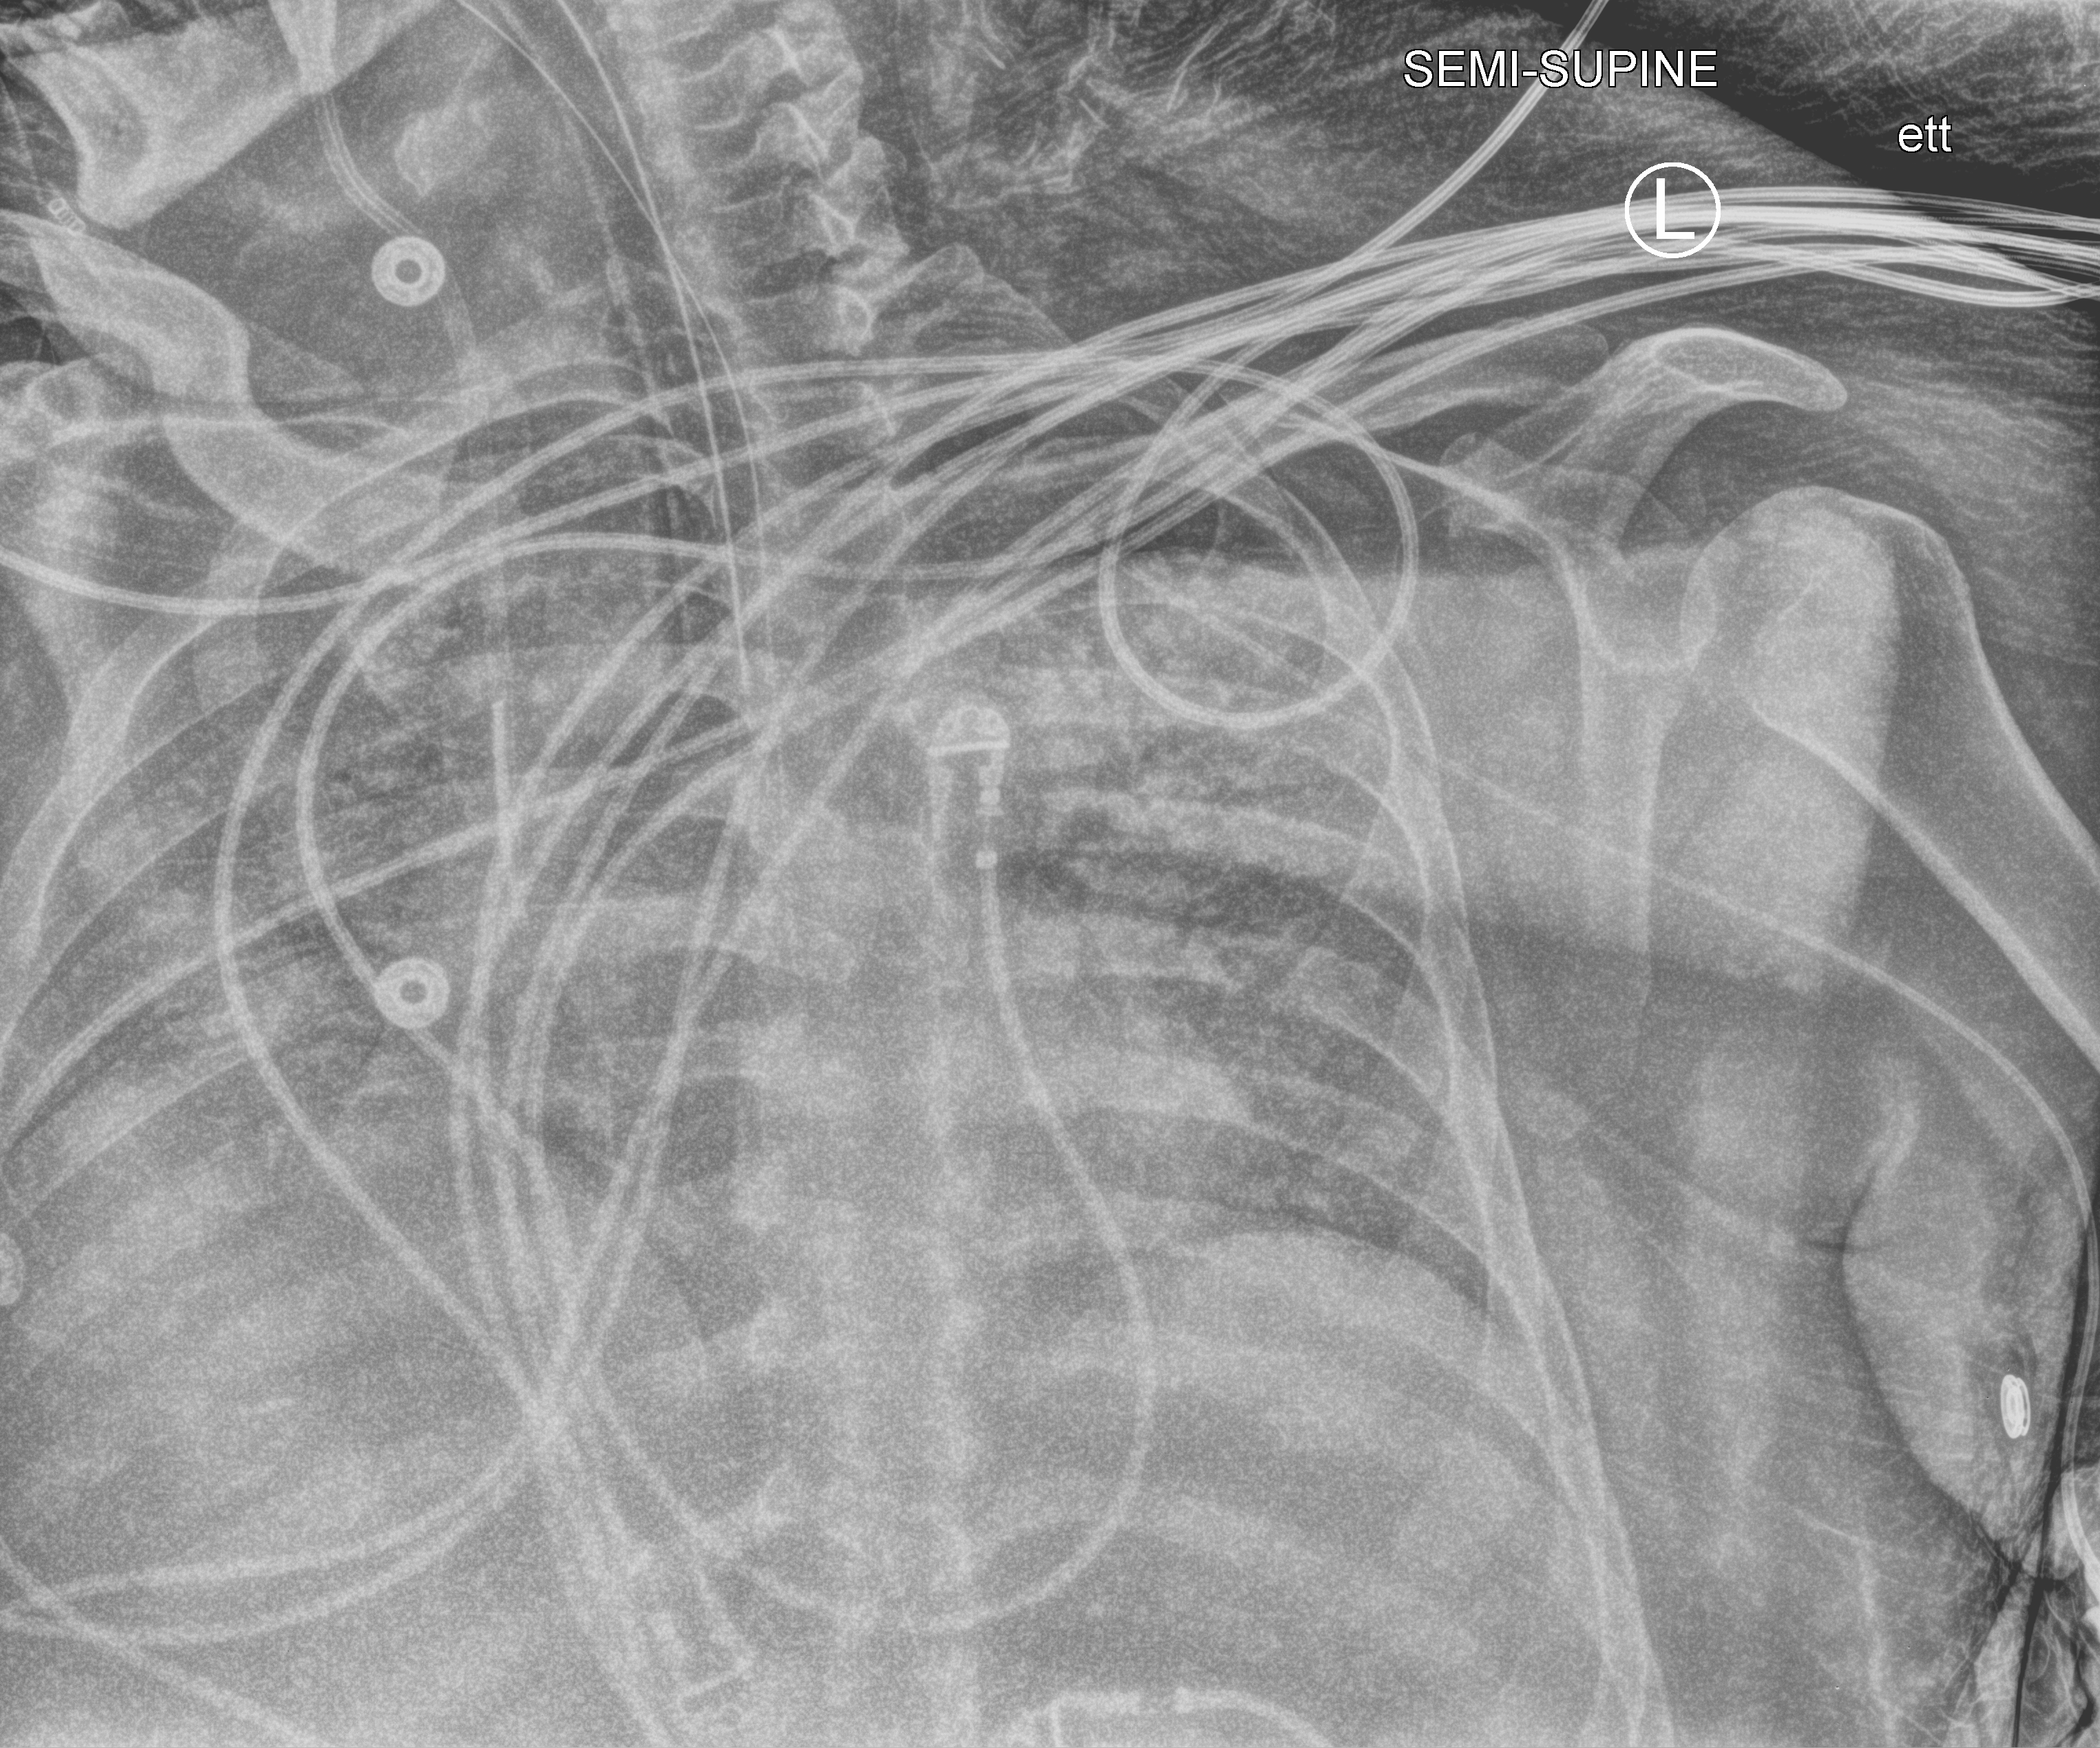
Bedside chest radiograph (computed radiography), anteroposterior (AP) projection. Patient hospitalised with COVID-19, aged 18–59 years.
Hospital-stay facts (about this admission, not read from this image; timing relative to this image not recorded):
- mechanically ventilated during this hospital stay: yes